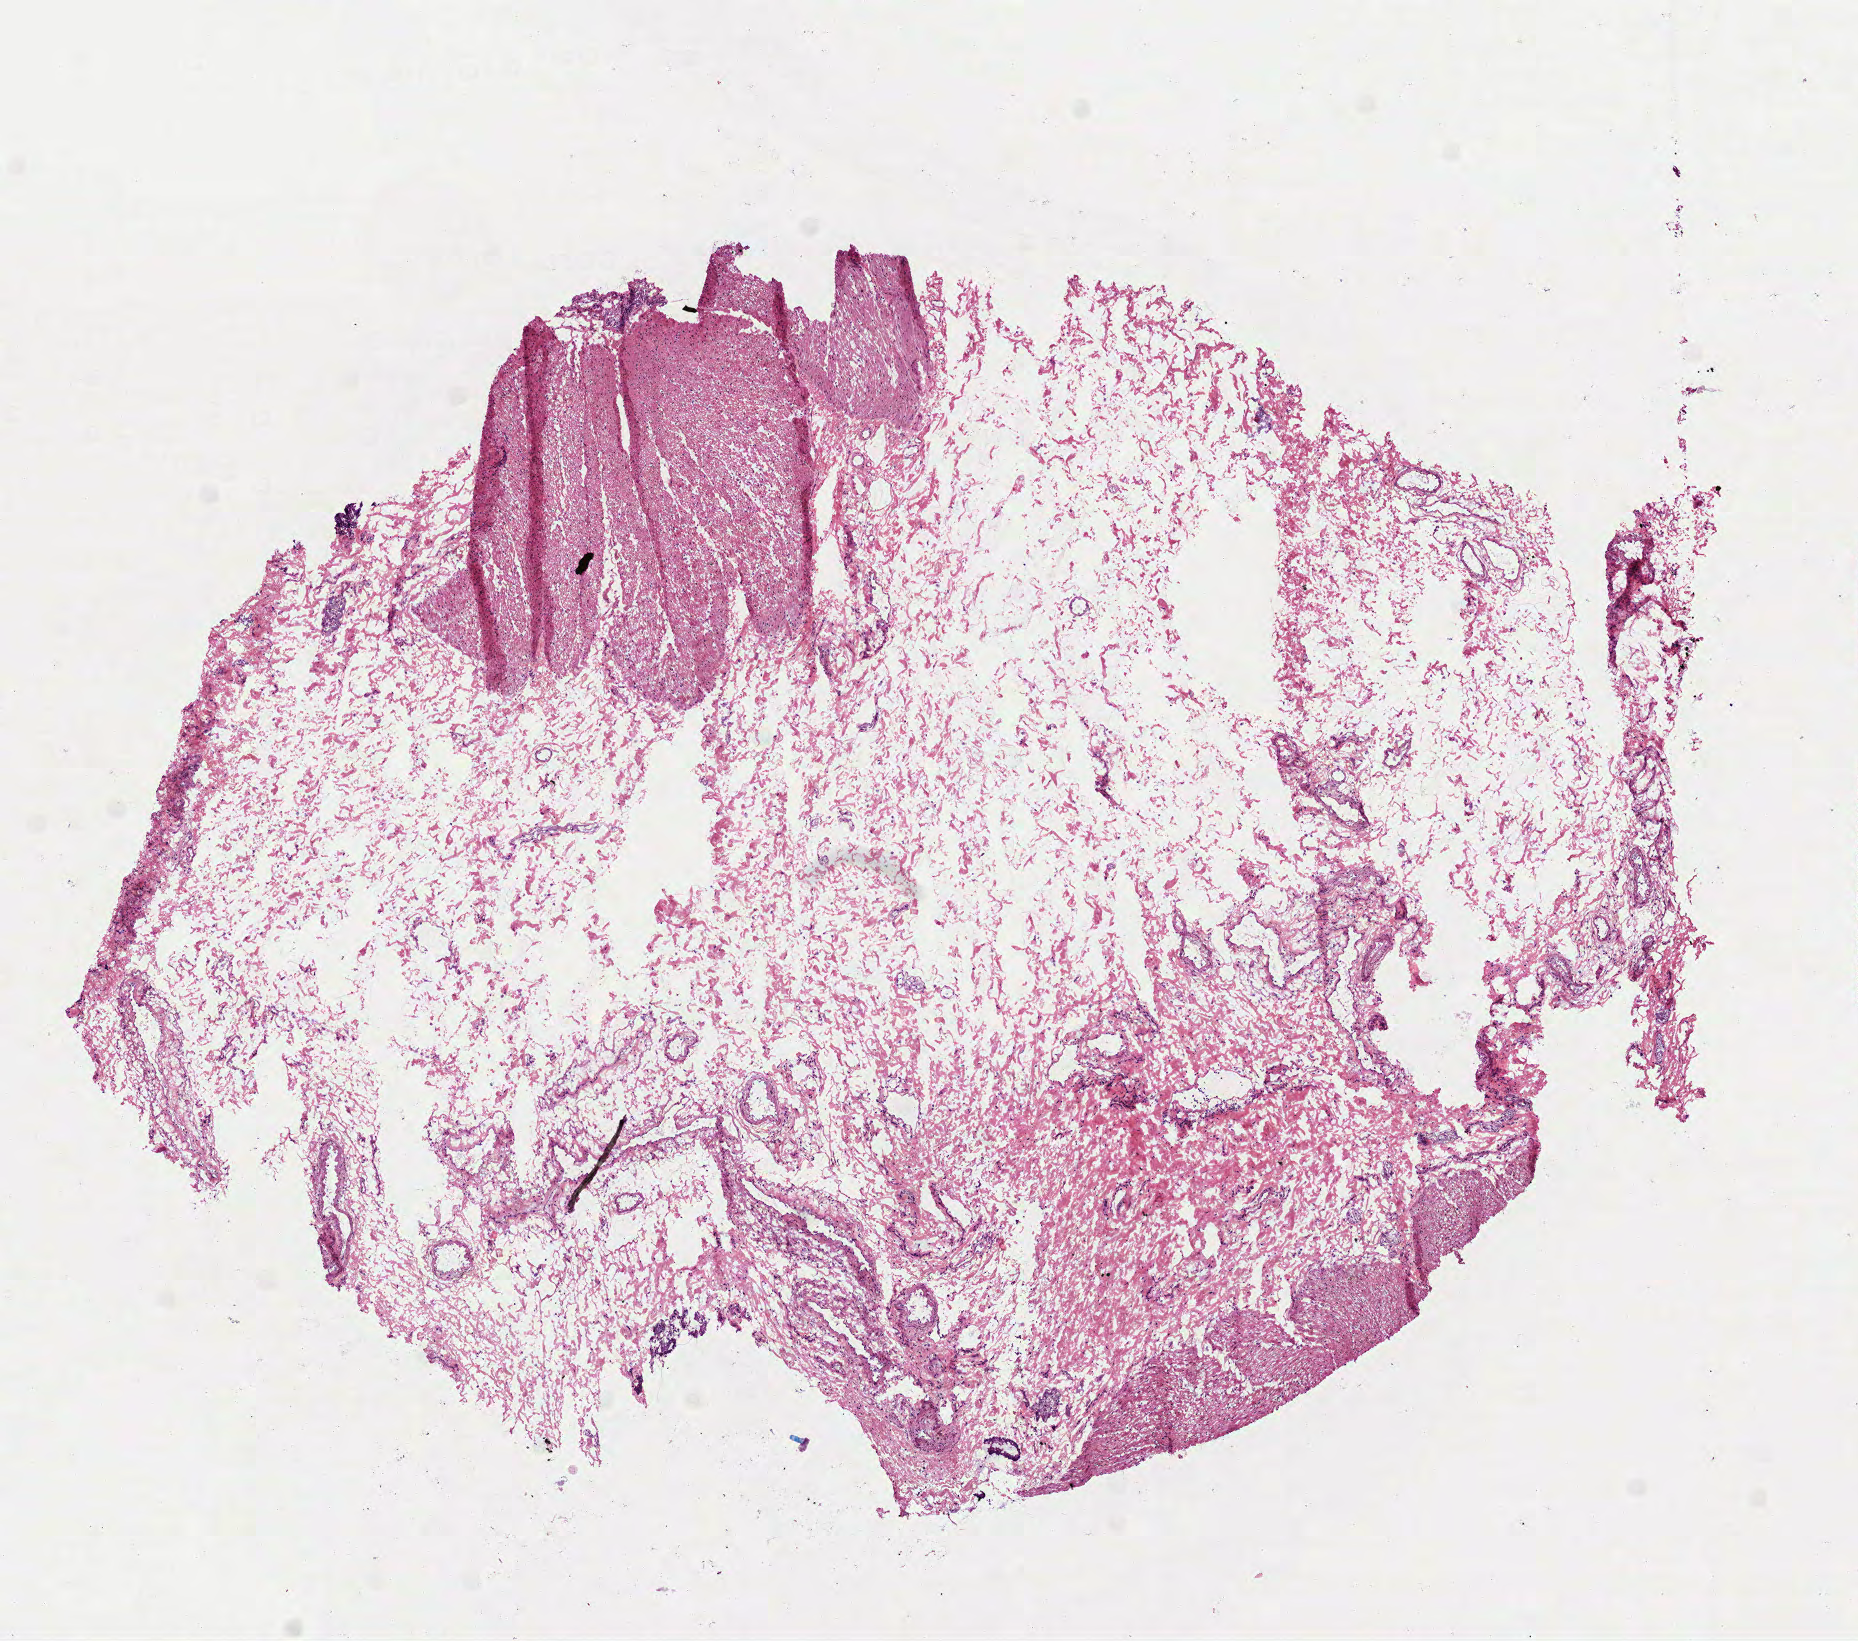
Whole-slide histology image, Hematoxylin and eosin (H&E) stained, whole scanned area (about 7.5 x 6.6 mm, slide scanned at 40x) shown as a low-resolution overview, frozen section from the top of the tissue portion, rectum, solid tissue normal (non-tumour tissue) sample. Female, age 79 years at initial diagnosis.
This section: solid tissue normal sample (biorepository sample class). Patient diagnosis: Adenocarcinoma, NOS.